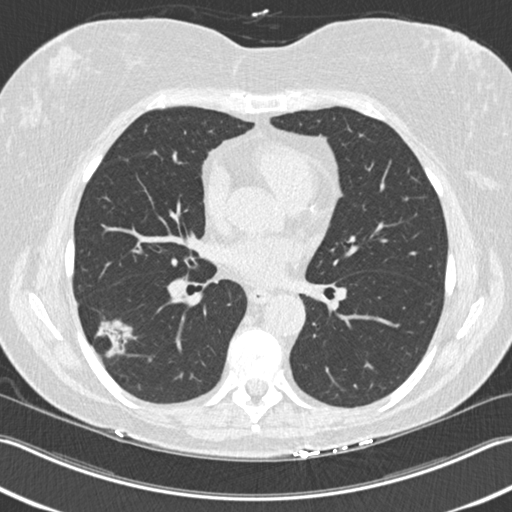
Chest CT (low-dose screening protocol), one axial image. Baseline annual screen. Lung window (W 1500 / L -600 HU). 2 mm slice thickness. Standard (soft-tissue) reconstruction kernel (B30f). 120 kVp. Female, age 63 years at enrolment. Current smoker at enrolment.
Lesion marked by an expert reader, bounding box <78,315,140,371> (left, top, right, bottom; pixels). The screening reader recorded 3 non-calcified nodules or masses ≥4 mm on this exam; which of them this box marks is not recorded. Official screen result: positive, change unspecified: nodule(s) >= 4 mm or enlarging nodule(s), mass(es), or other non-specific abnormalities suspicious for lung cancer. Lung cancer was diagnosed 57 days after this screen: bronchiolo-alveolar adenocarcinoma, NOS, right lower lobe, well differentiated (G1), stage IA (AJCC 6th edition), 25 mm at pathology.